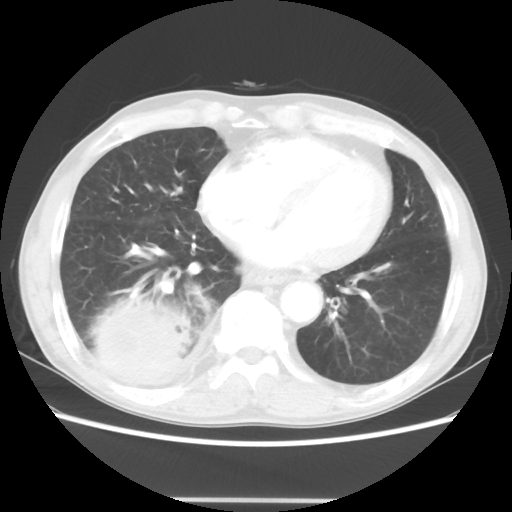
Chest CT, one axial slice; 100 kVp; lung window (W 1500 / L -600 HU); 512 × 512 image matrix, field of view 361 × 361 mm. Male patient, age 66 years. Case-level facts recorded for this patient, not image findings: clinical TNM (as recorded): T4 N1 M1.
Annotated regions visible in this slice (rectangle marked by the reading radiologist):
- lung tumour (recorded histology: small cell carcinoma): bounding box (x1, y1, x2, y2) in pixels: (84, 289, 200, 401)